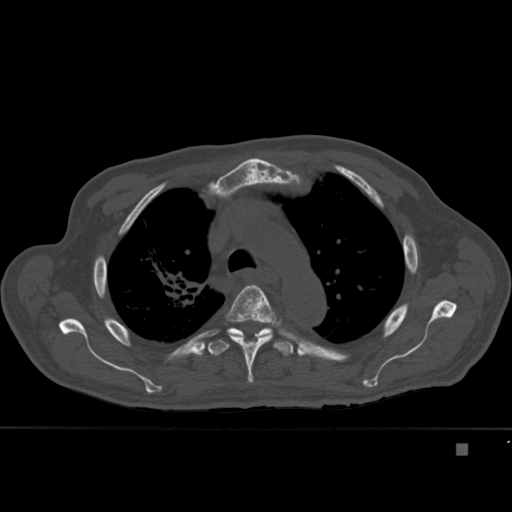
CT including the spine, one axial slice. Position 317 of 451 along the scan axis. Bone window (W 1800 / L 400 HU). 1.5 mm slice thickness. 512 × 512 image matrix, field of view 378 × 378 mm. Male patient, age 75 years. Case-level facts recorded for this patient, not image findings: primary cancer: prostate.
Annotated regions visible in this slice (semi-automatic segmentation, software-assisted and operator-edited):
- T4 vertebra: bounding box <225,284,279,383> (left, top, right, bottom; pixels)
- T5 vertebra: <208,328,293,356>